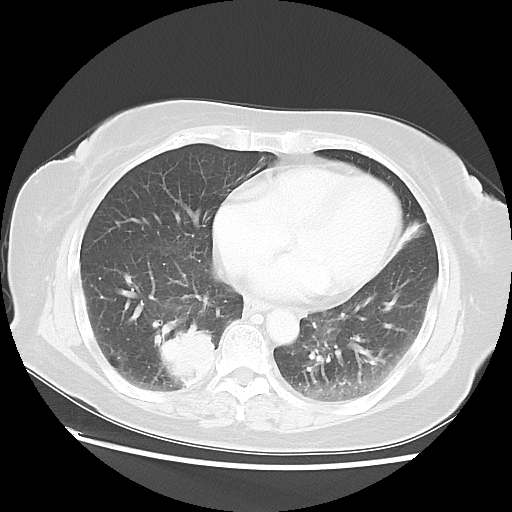
Chest CT, one axial slice. Position 22 of 52 along the scan axis. 120 kVp. Lung window (W 1500 / L -600 HU). 5 mm slice thickness. 512 × 512 image matrix, field of view 356 × 356 mm. Female patient, age 69 years. Case-level facts recorded for this patient, not image findings: clinical TNM (as recorded): T2 N1 M1a.
Structures marked on this image (bounding box drawn by a radiologist):
- lung tumour (recorded histology: adenocarcinoma): box from (x=152, y=321) to (x=220, y=386) px